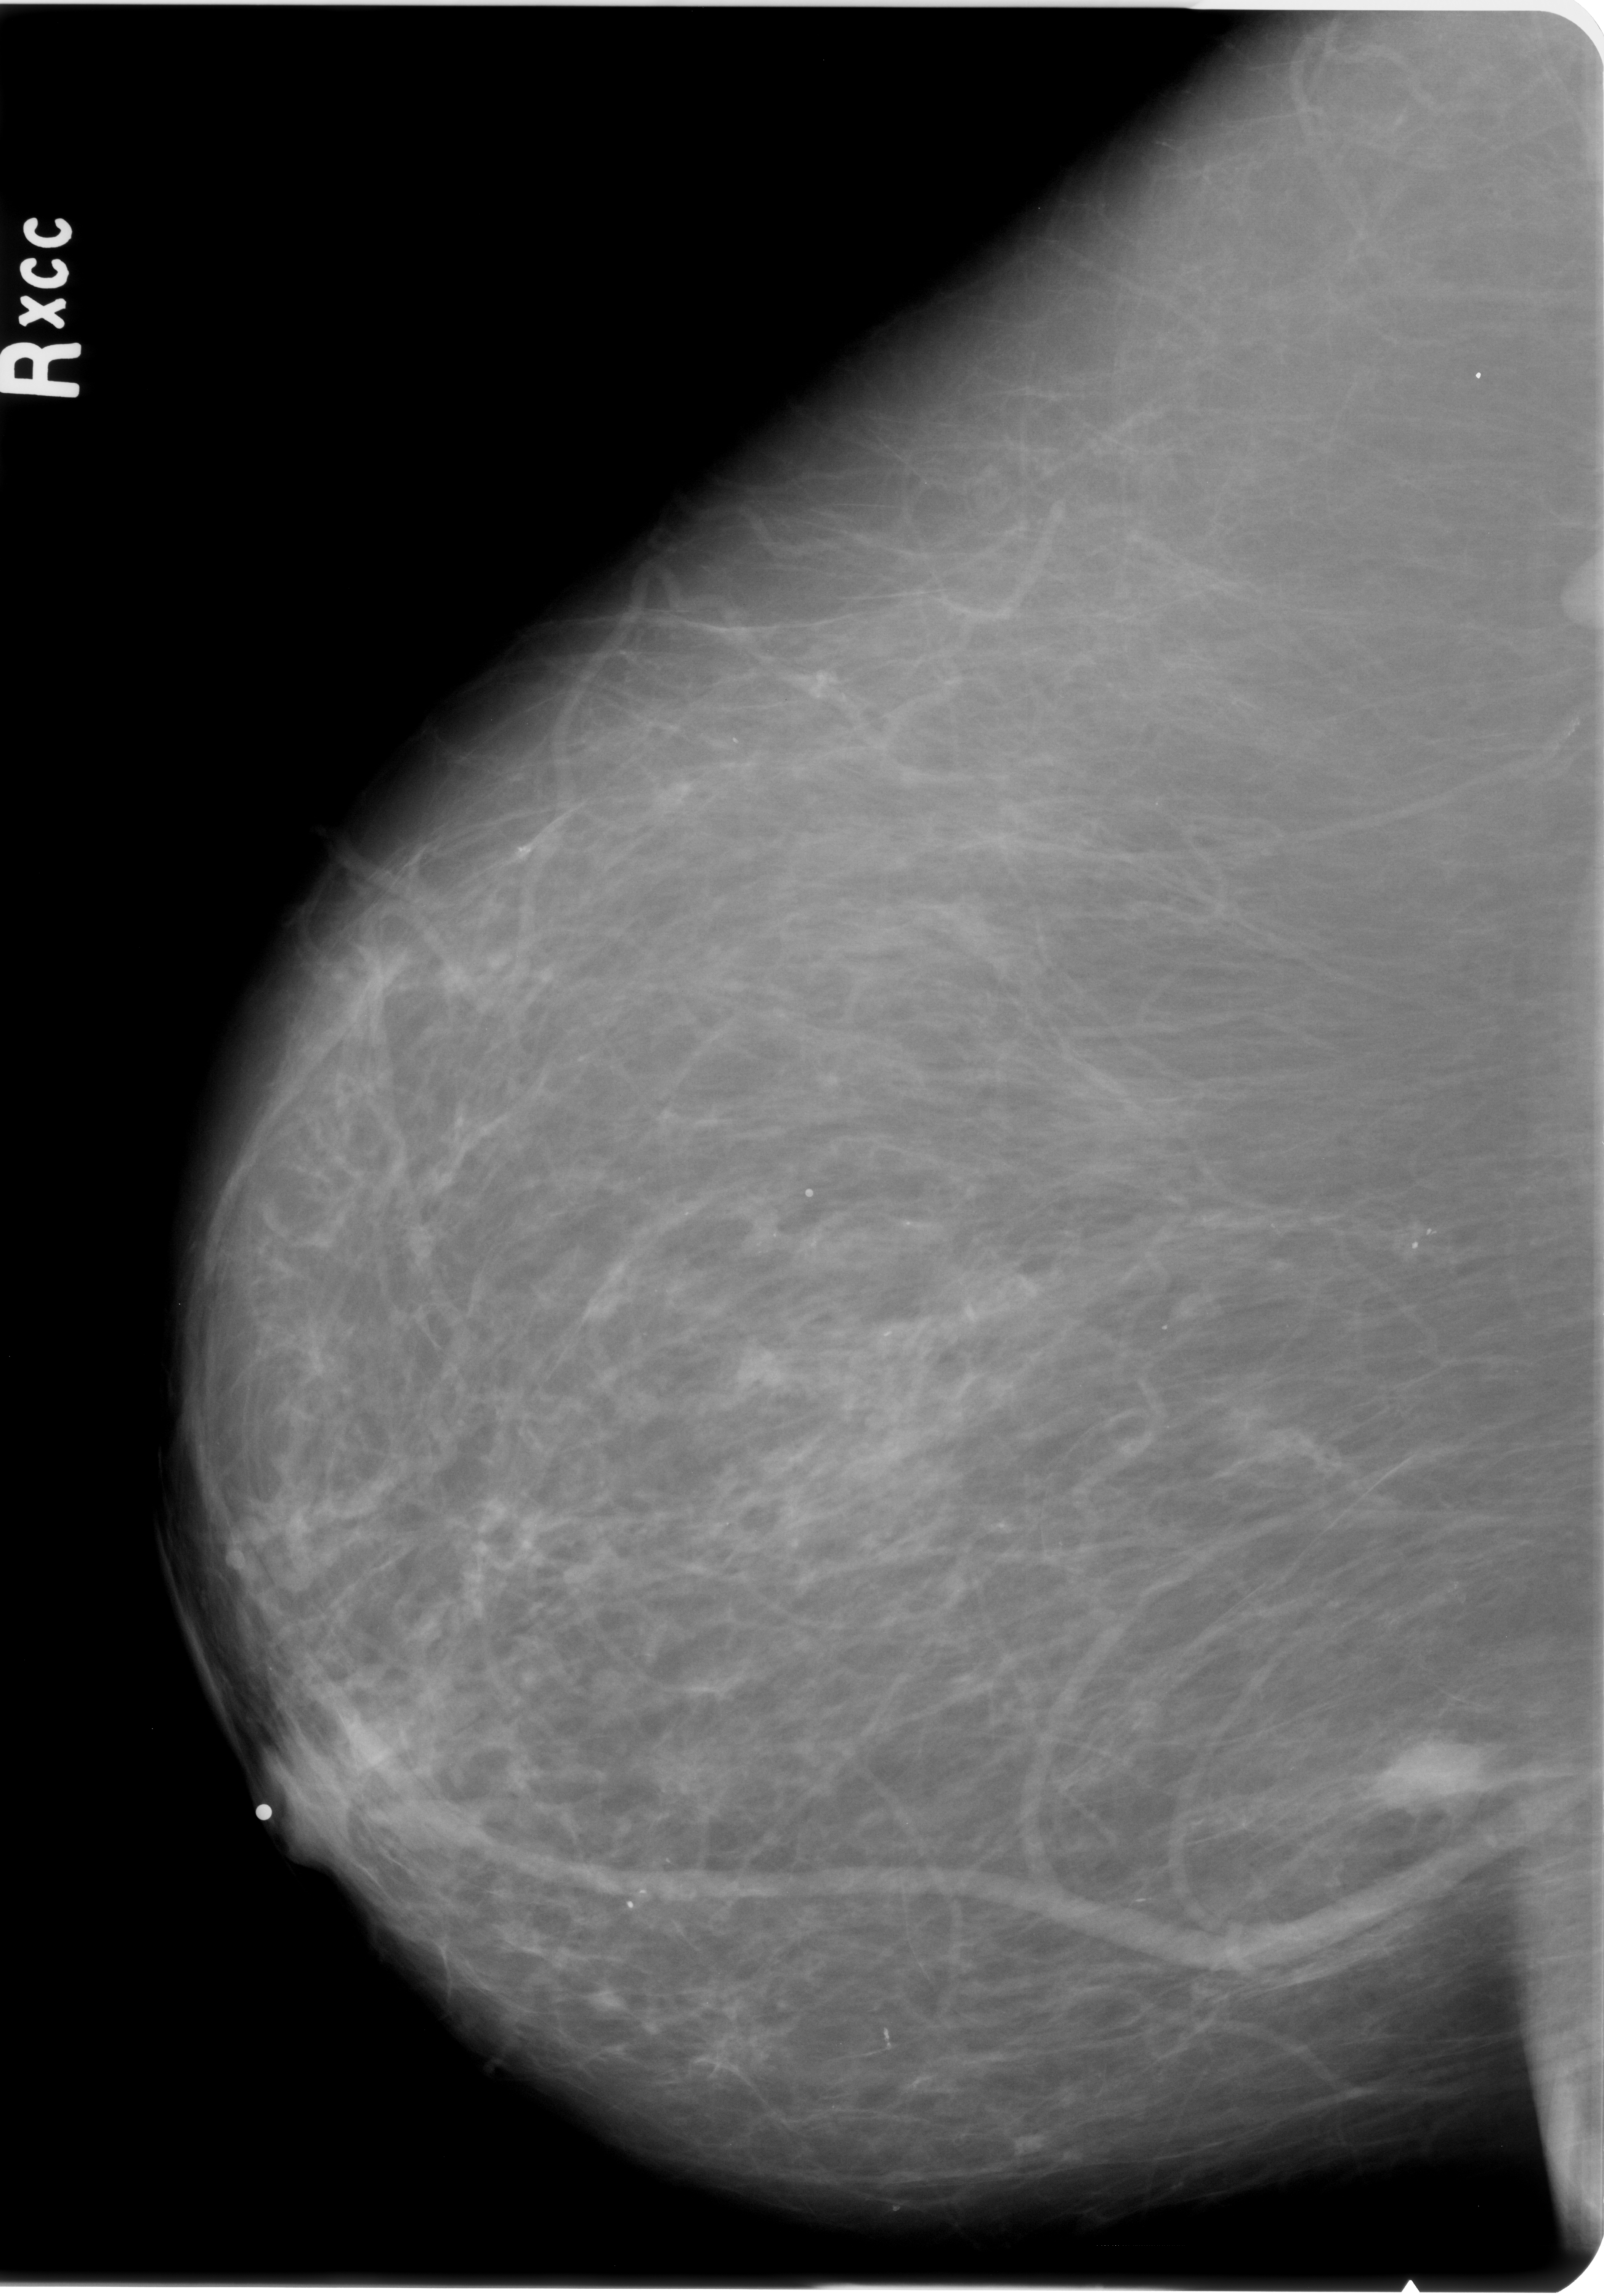
Digitized screen-film mammogram. Right breast. CC view. Breast composition: scattered fibroglandular densities (BI-RADS density category 2 of 4). 1604 × 2296 image matrix.
Marked abnormalities (boxes around the expert regions of interest):
- mass, shape irregular, margins spiculated; BI-RADS assessment category 4; subtlety rating 5 on a 1 (subtle) to 5 (obvious) scale; pathology (as recorded): malignant: bounding box <1369,1730,1480,1819> (left, top, right, bottom; pixels)